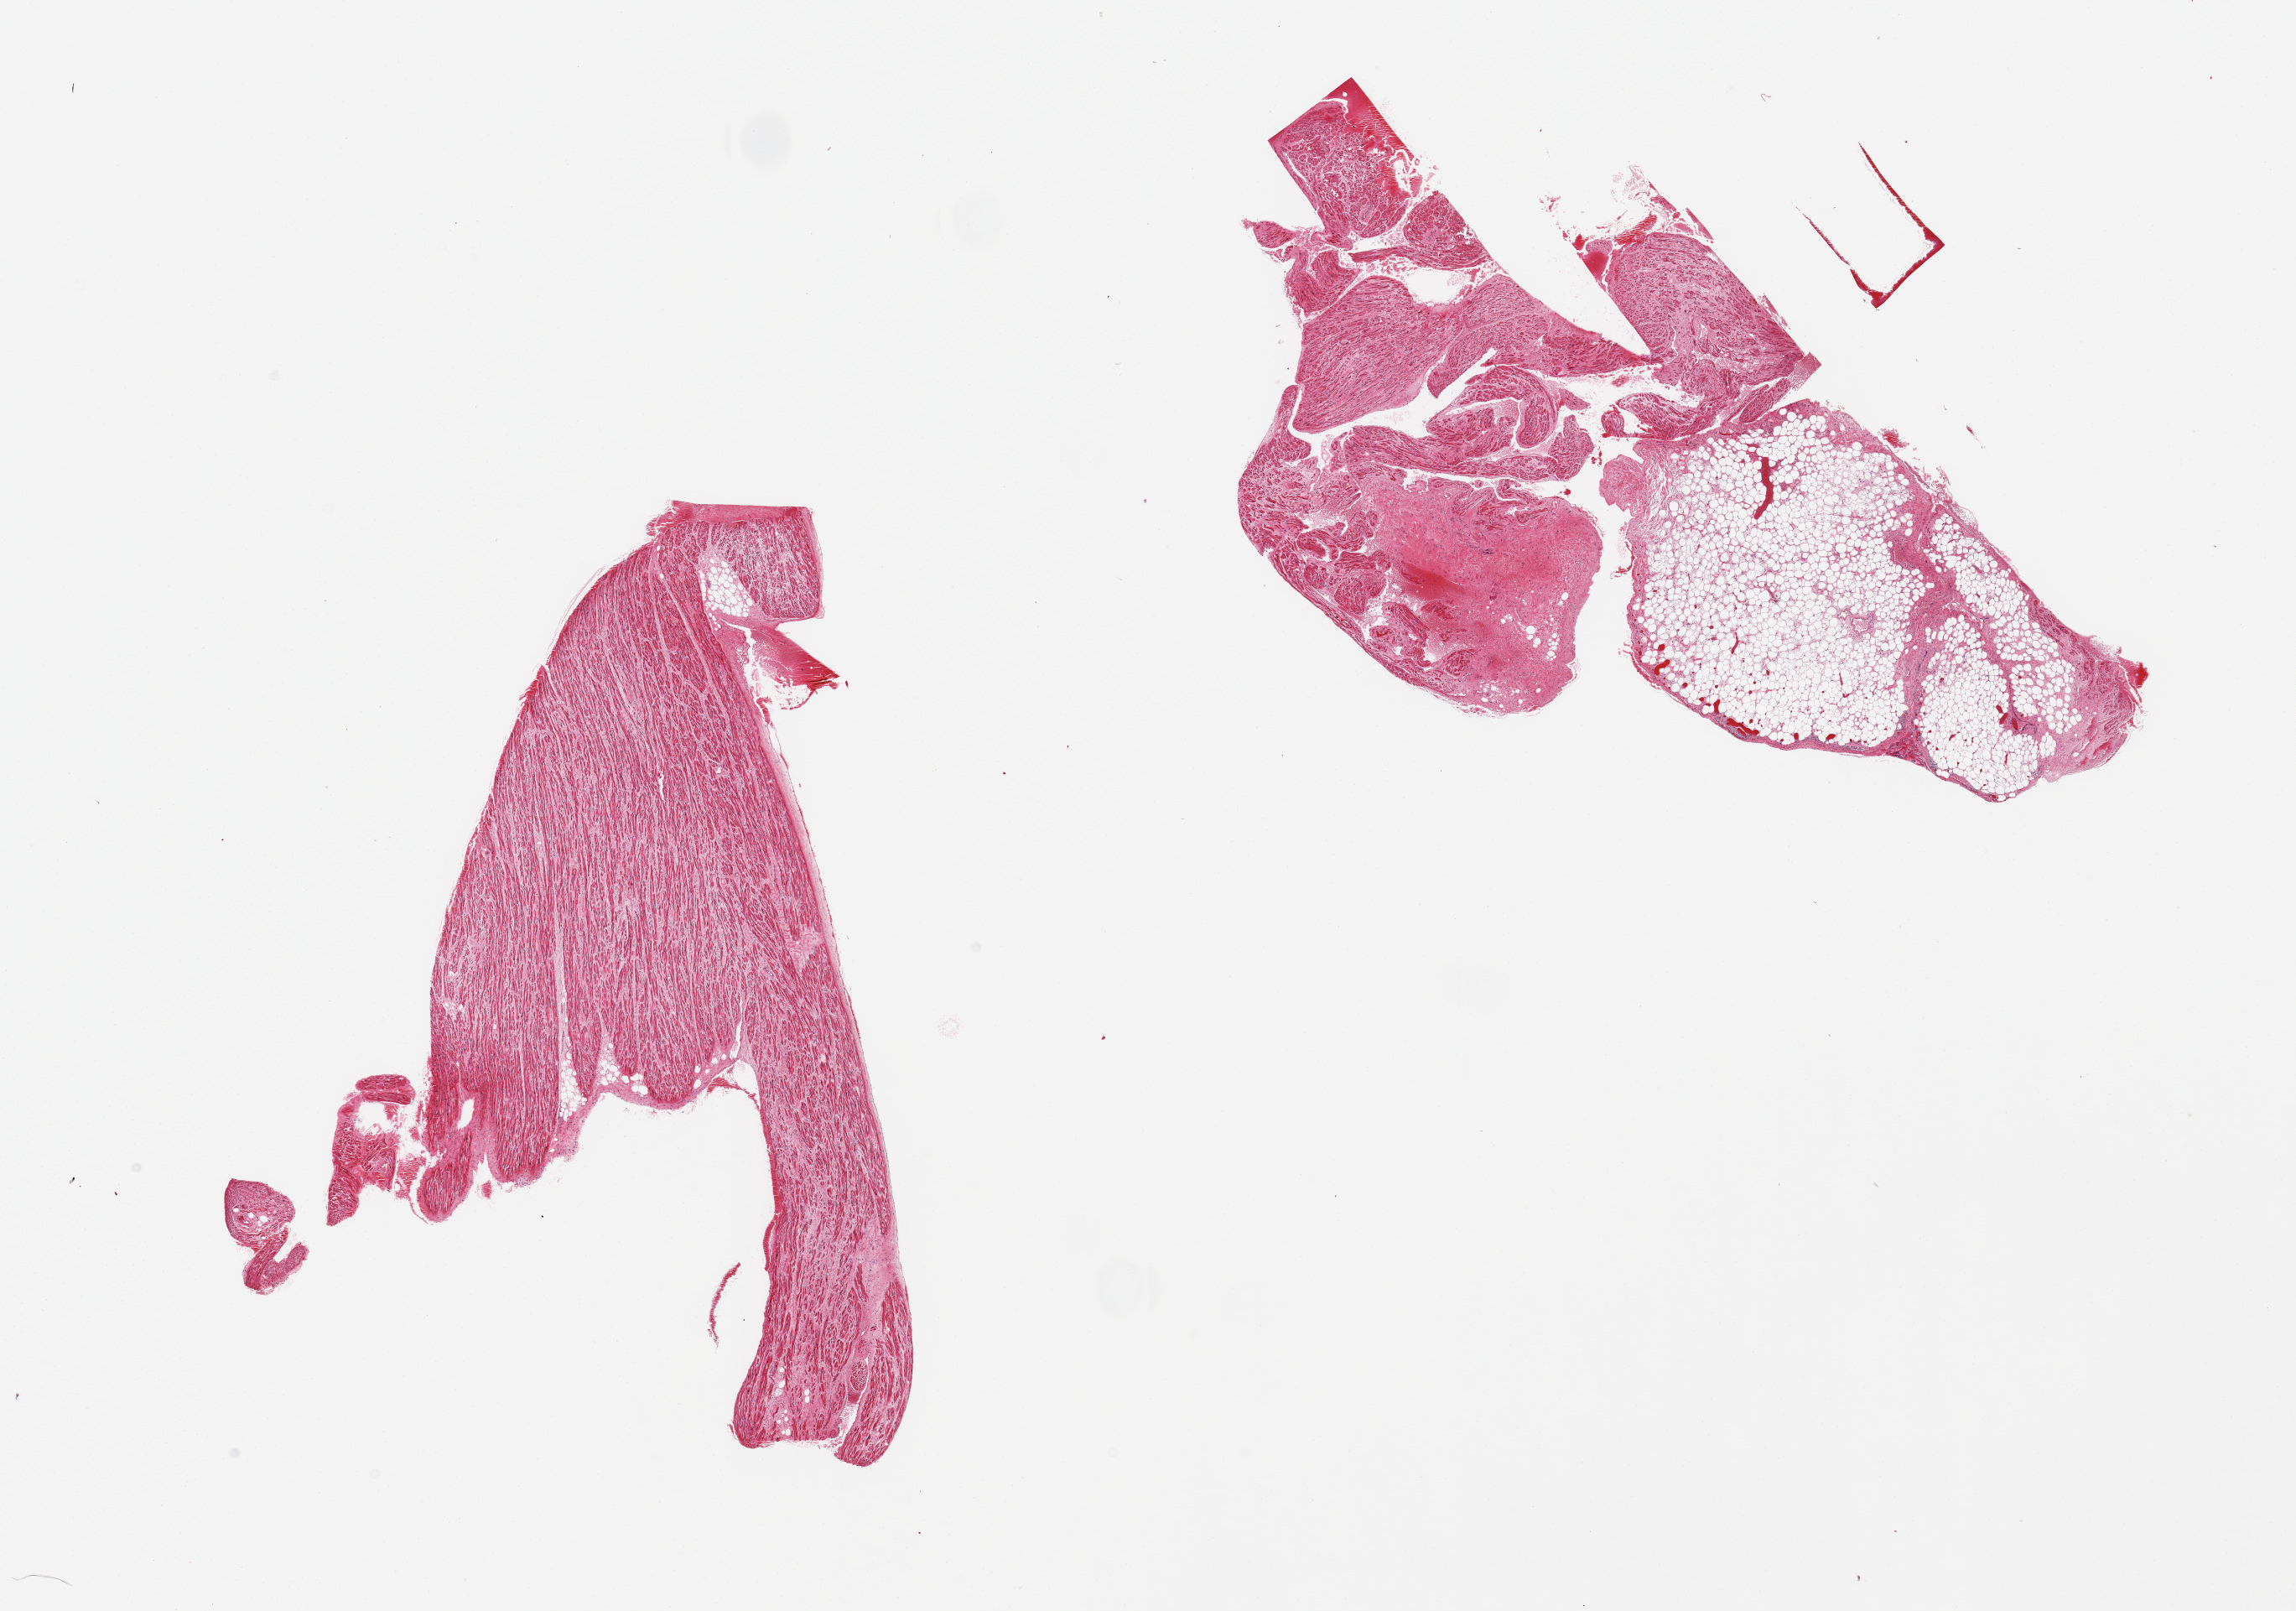
Whole-slide image, hematoxylin and eosin (H&E) stain, brightfield — a low-resolution overview of the entire scanned area, about 21.7 x 15.2 mm (acquisition: 20x scan); PAXgene-fixed paraffin-embedded (PFPE) section; target tissue: auricular appendage; tissue donor sample. Female donor.
Reviewer comment on this tissue sample: 2 pieces, 1 with 50% fat.